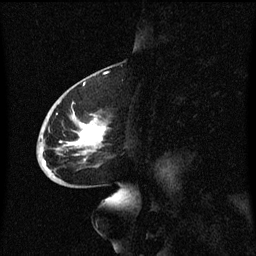
Breast MRI (dynamic contrast-enhanced), one sagittal slice; slice 33 of 60 in the series (ordered by position); dynamic contrast-enhanced series, image 2 of 3 at this slice position (ordered by acquisition); 1.5 T; TE 4.2 ms, TR 8.4 ms; 256 × 256 image matrix. Female patient, age 68 years. From the clinical record (not read from this slice): setting: breast cancer imaged before/during neoadjuvant chemotherapy; receptor status: triple-negative.
Outlined on this slice (semi-automatic segmentation, software-assisted and operator-edited):
- analysis volume of interest (the breast-tissue region the enhancement analysis was run in; not a lesion): bounding box <38,94,113,173> (left, top, right, bottom; pixels)
- tumour enhancement mask (voxels above the 70 % enhancement threshold inside the analysis volume of interest): <42,116,107,171>